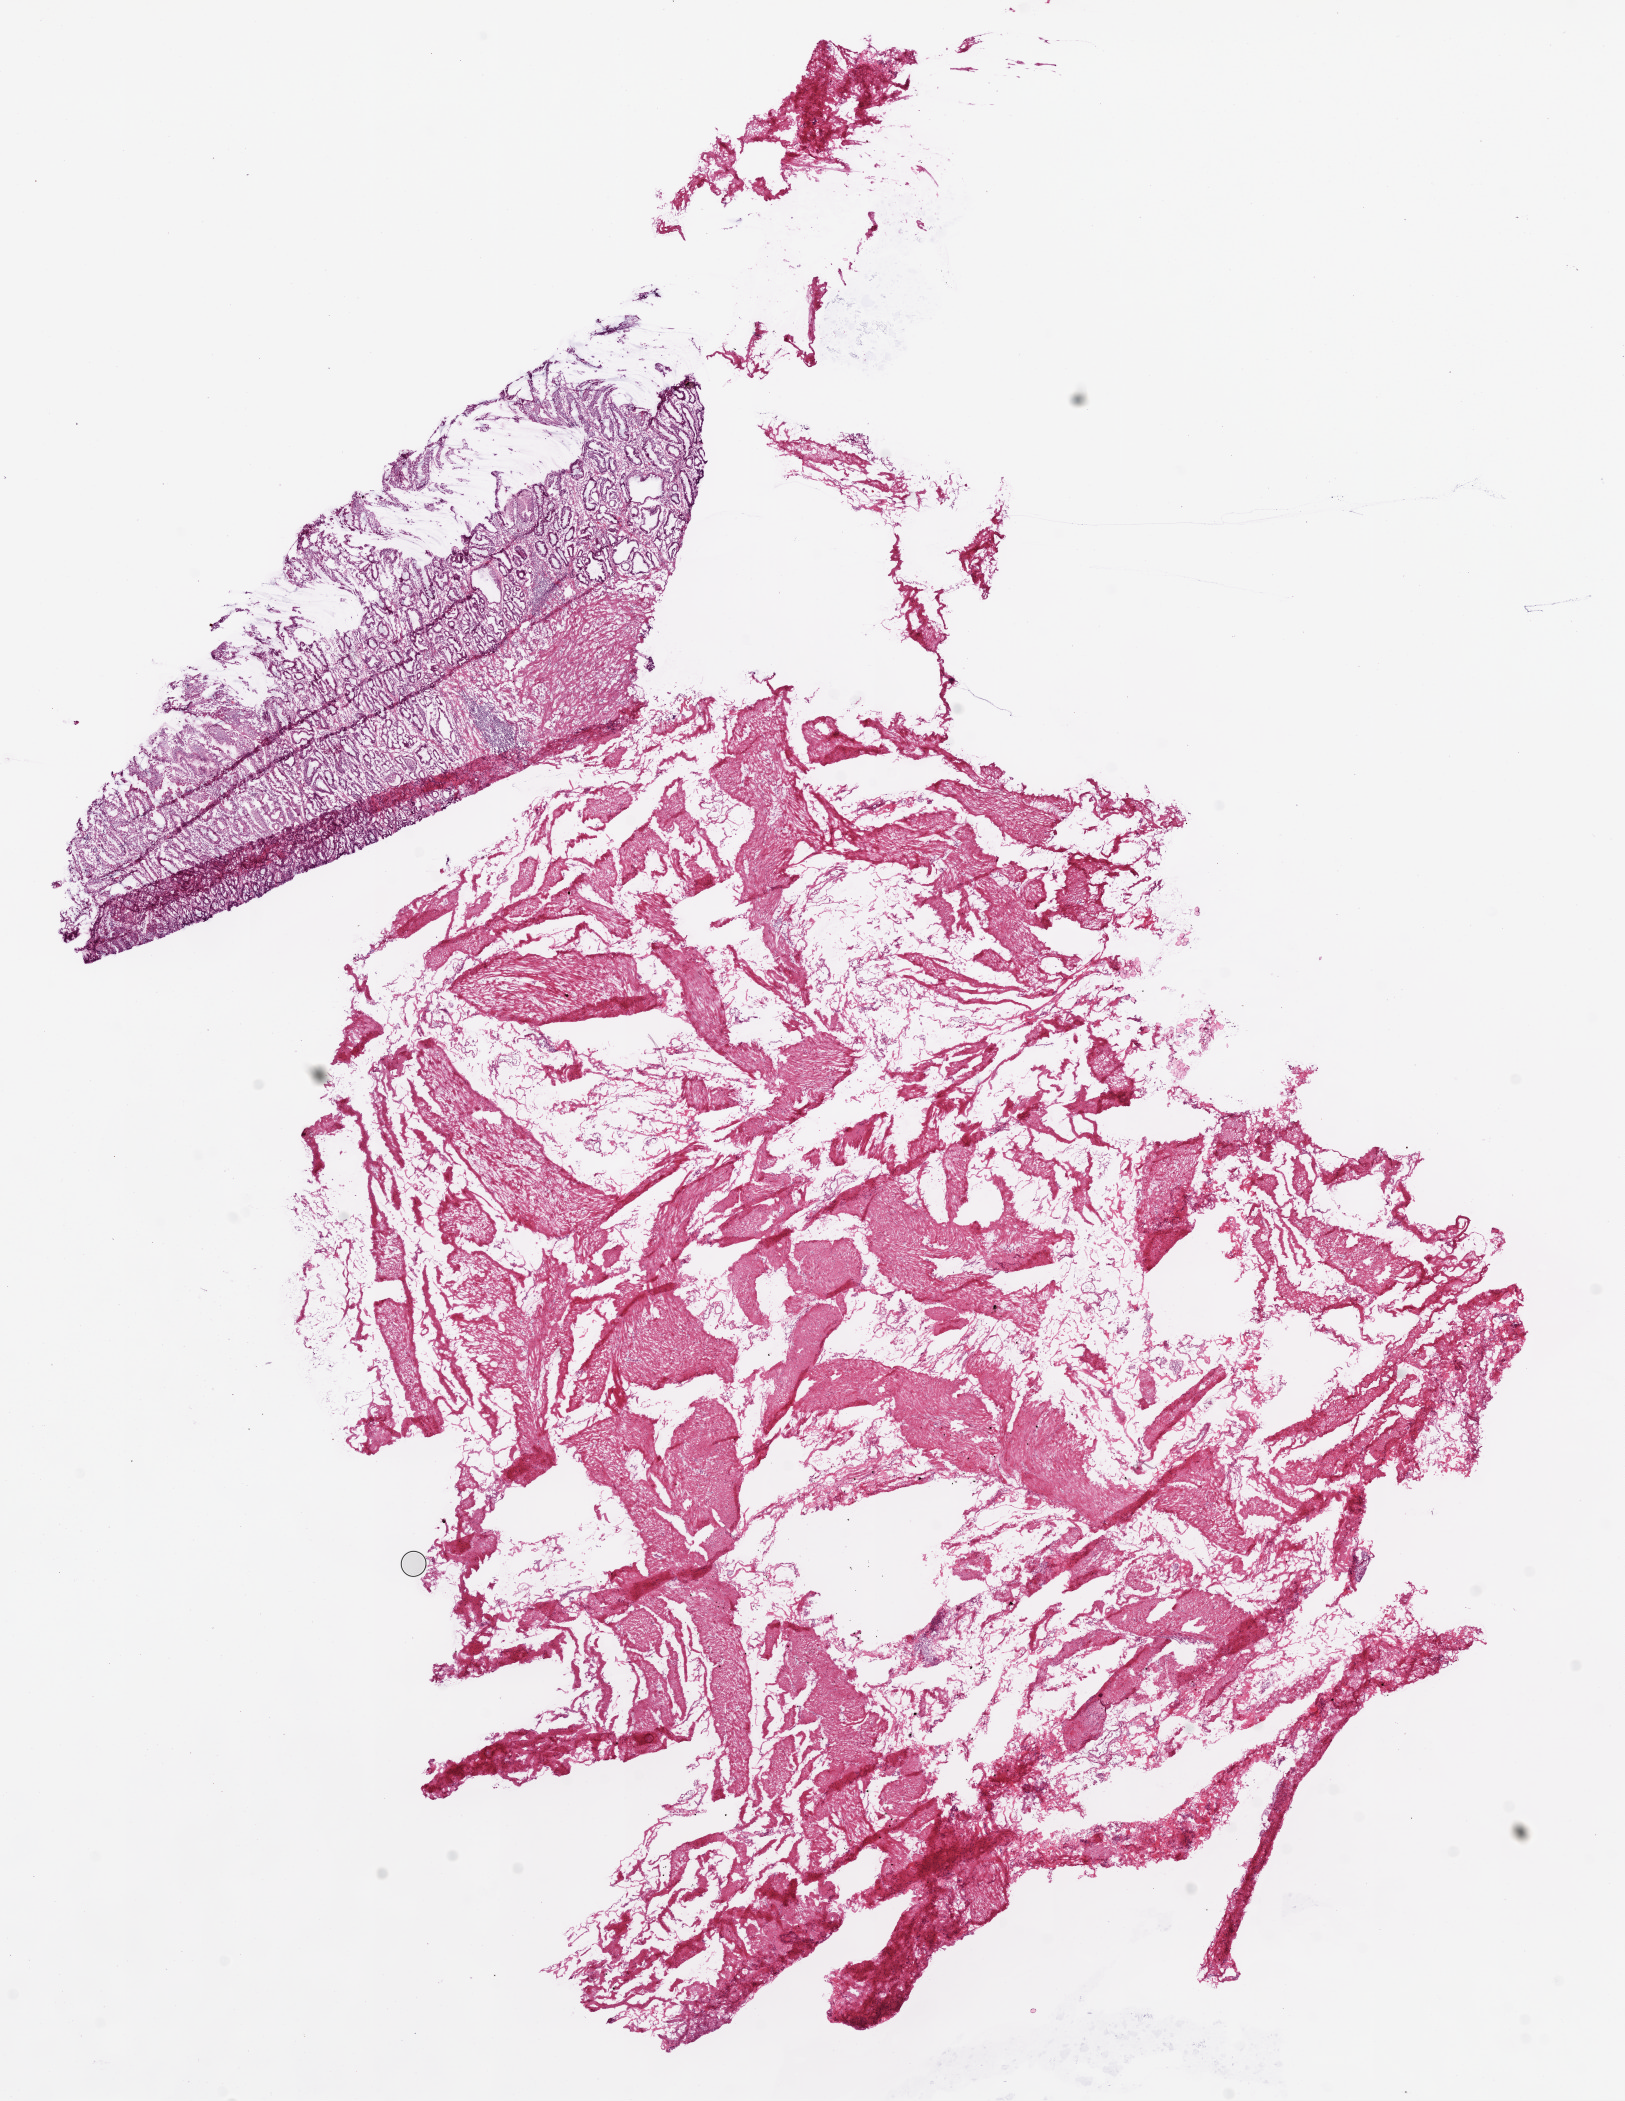
Digitized Hematoxylin and eosin (H&E) stained tissue section (whole slide) — whole scanned area (about 13.0 x 16.9 mm, slide scanned at 20x) shown as a low-resolution overview, frozen section from the top of the tissue portion, stomach, solid tissue normal (non-tumour tissue) sample. Female, age 78 years at initial diagnosis.
• this section: solid tissue normal sample (biorepository sample class)
• patient diagnosis: Adenocarcinoma, NOS